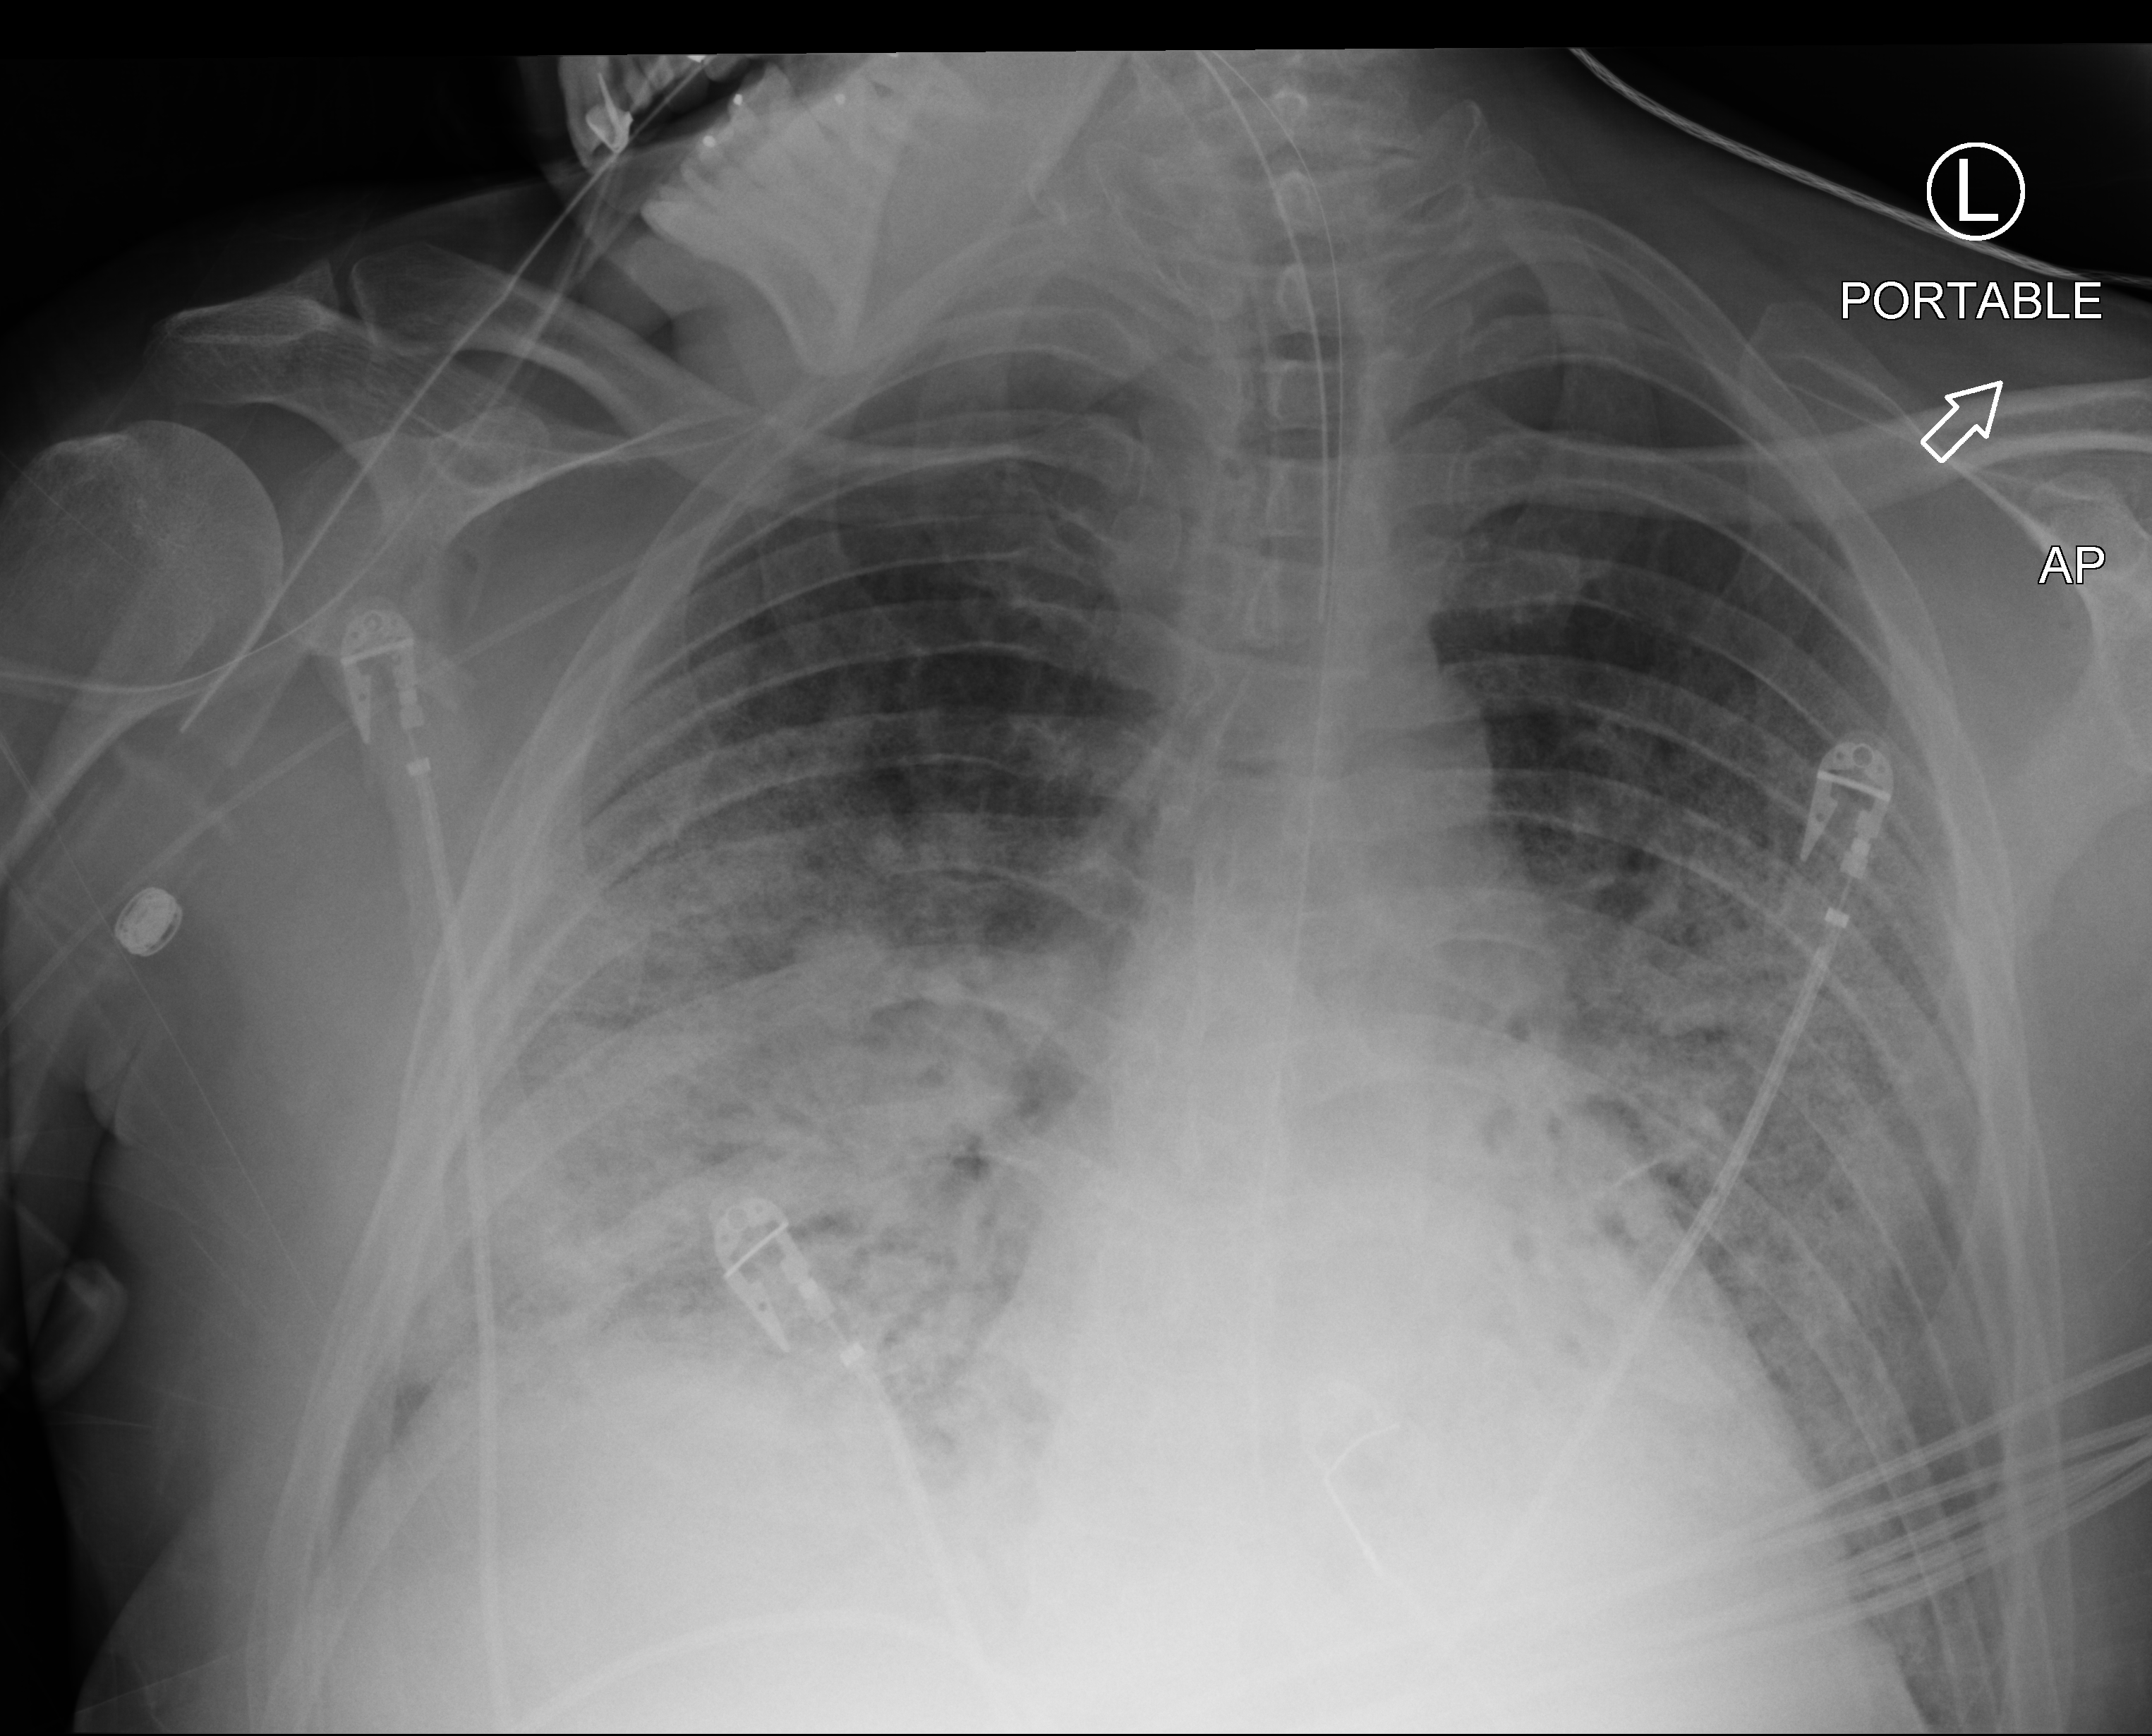
Bedside chest radiograph (computed radiography), anteroposterior (AP) projection. Patient hospitalised with COVID-19; male, aged 18–59 years.
Hospital-stay facts (about this admission, not read from this image; timing relative to this image not recorded):
- smoking status (admission record): never